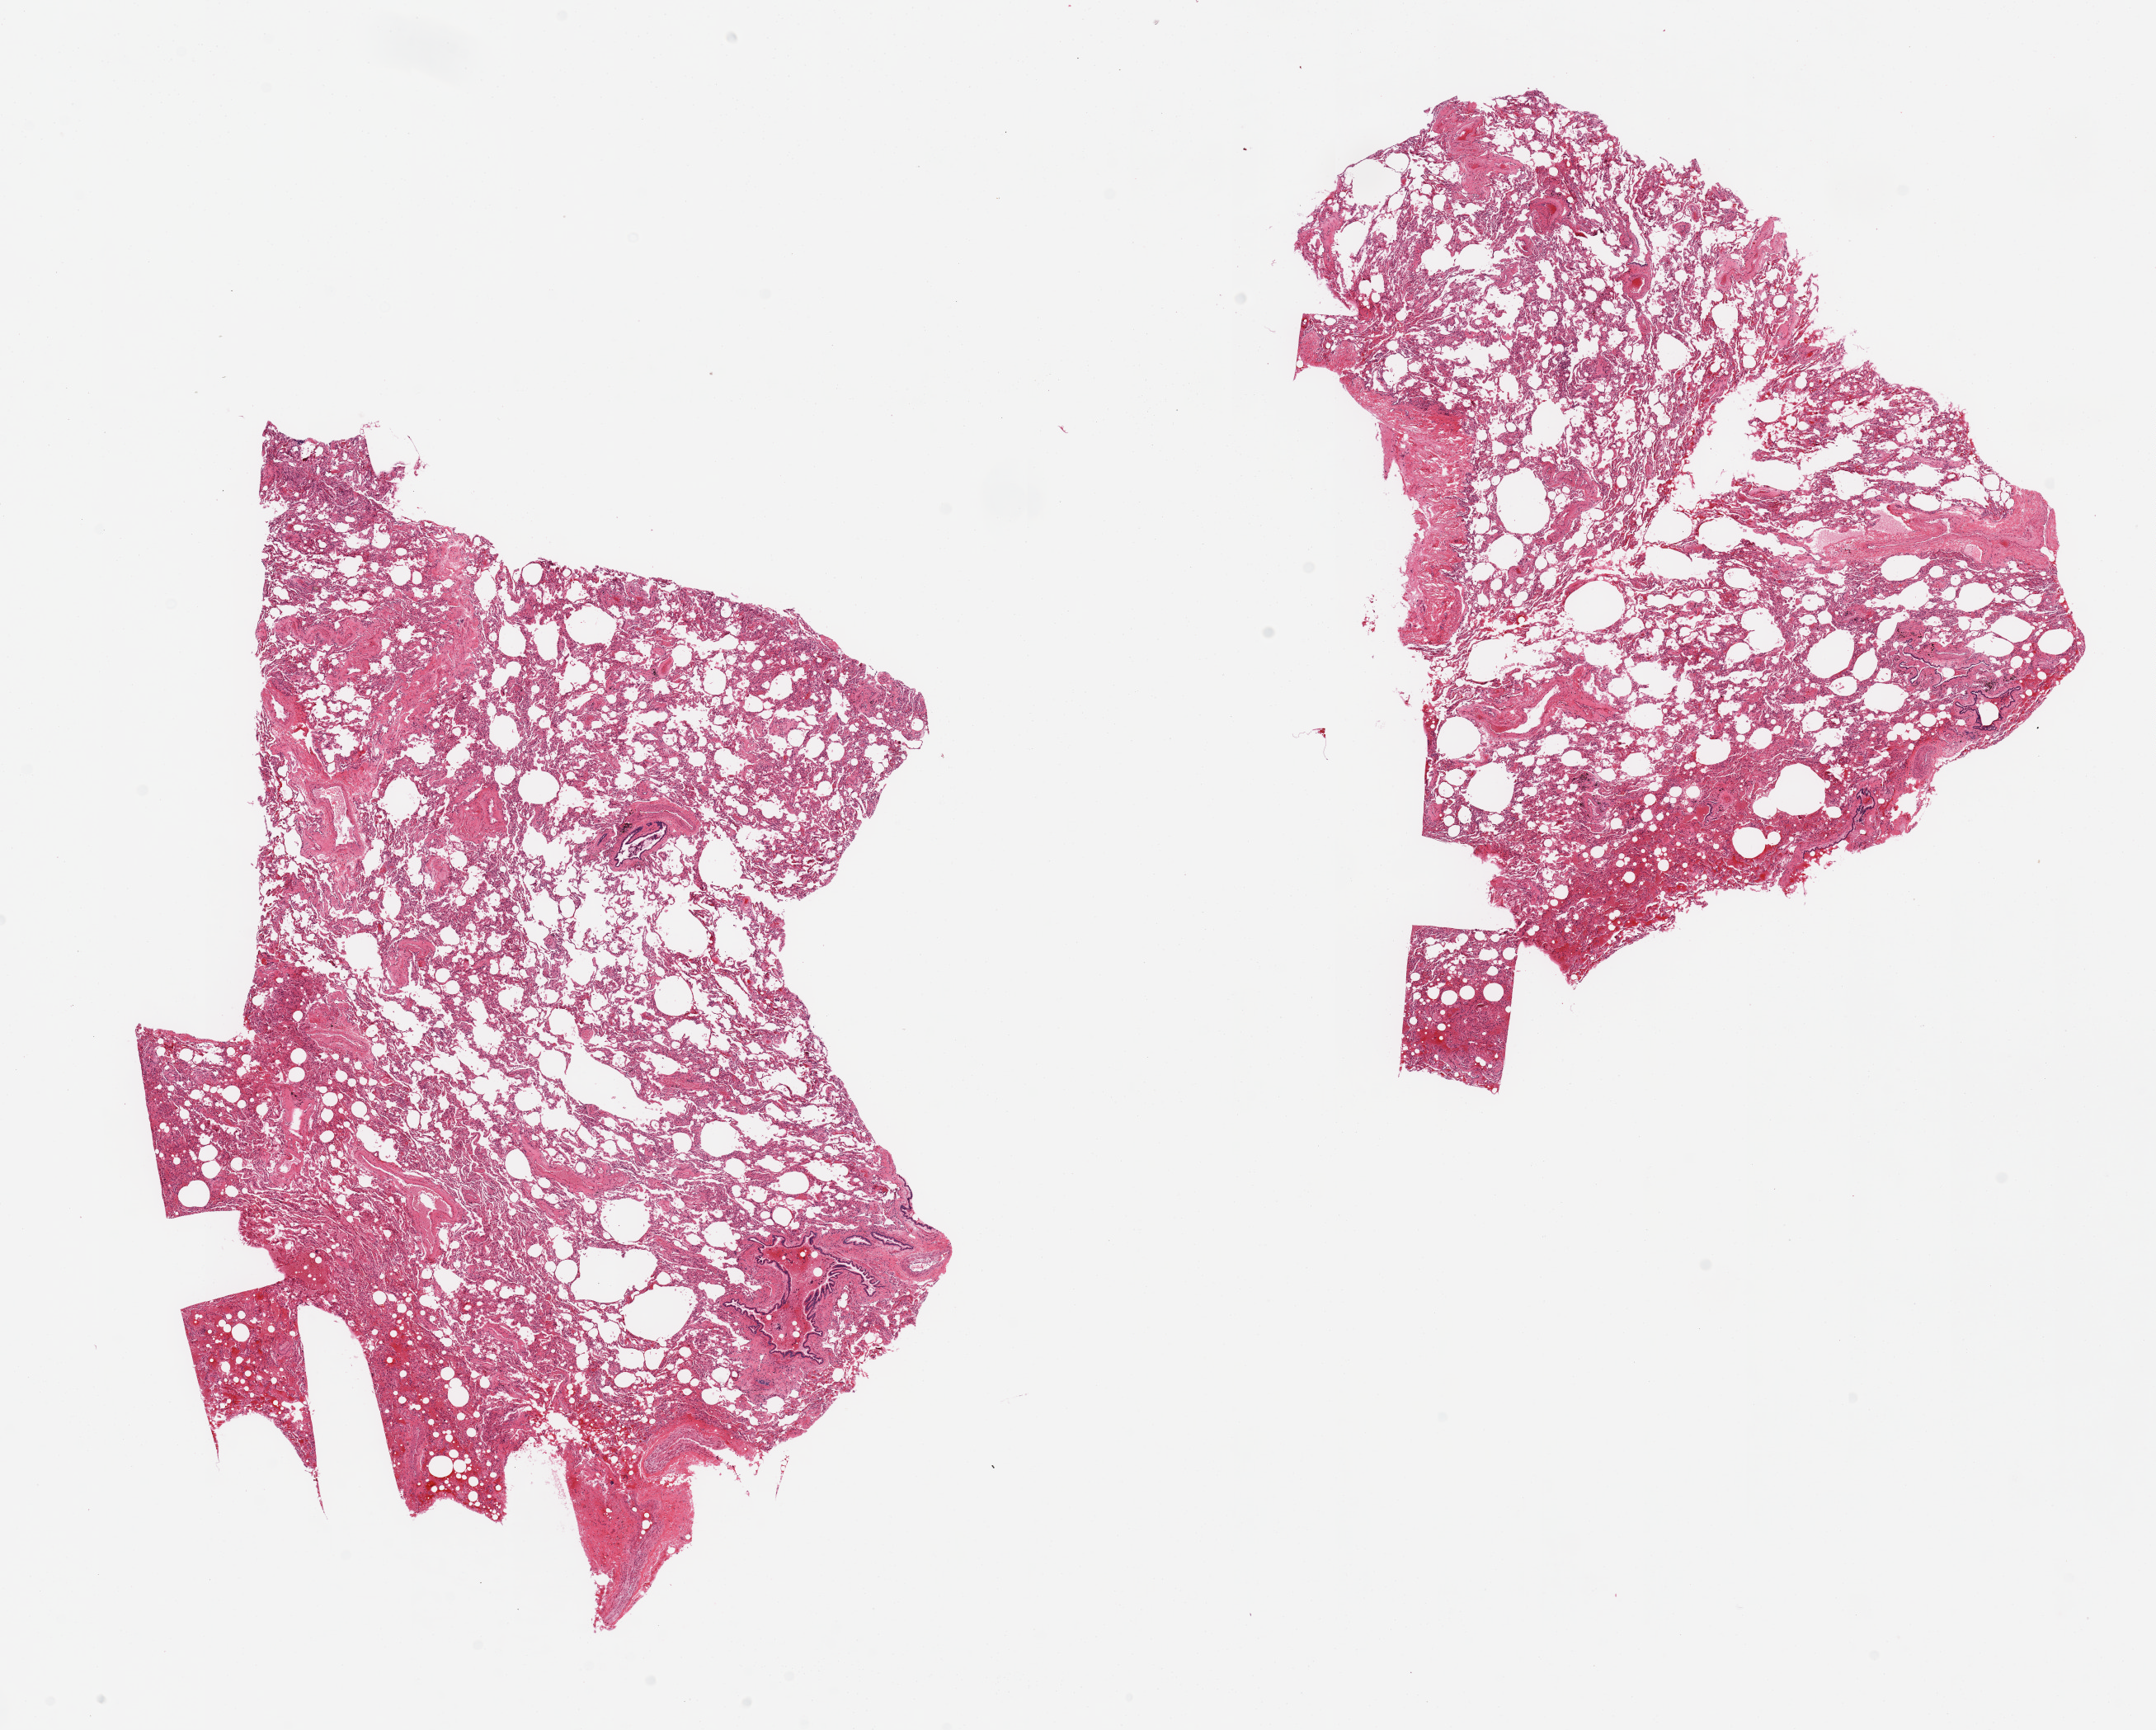
H&E whole-slide image — whole scanned area (about 20.7 x 16.6 mm) shown as a low-resolution overview; PAXgene-fixed, paraffin-embedded tissue; sampled site (target tissue): lung; donor tissue sample.
• review note (as recorded): 2 pieces, mild hylaline membrane deposition, mild-moderate emphysematous changes